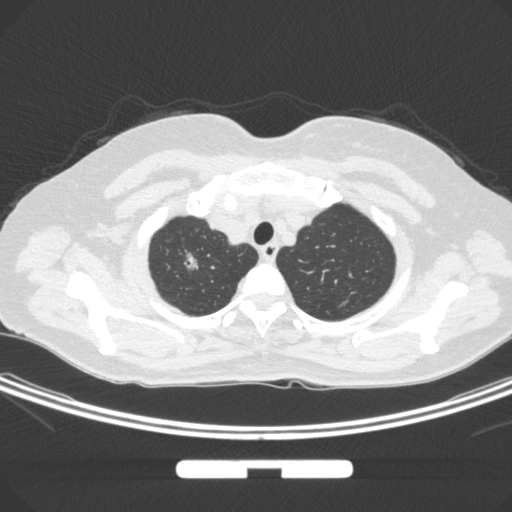
Chest CT, one axial slice. Position 256 of 295 along the scan axis. 120 kVp. Lung window (W 1500 / L -600 HU). 1 mm slice thickness. 512 × 512 image matrix, field of view 369 × 369 mm. Patient: female, 58 years. Case-level facts recorded for this patient, not image findings: clinical TNM (as recorded): T1b N0 M0.
Annotated regions visible in this slice (bounding box drawn by a radiologist):
- lung tumour (recorded histology: adenocarcinoma): bounding box [x1, y1, x2, y2] px = [172, 248, 206, 281]